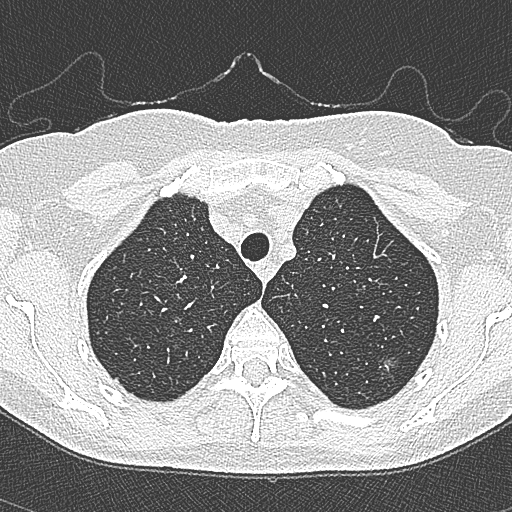
Low-dose screening chest CT, axial slice, second annual screen, lung window (W 1500 / L -600 HU), 1 mm slice thickness, lung (sharp) reconstruction kernel (B80f), 512 × 512 image matrix. Female, age 65 years at enrolment.
Expert reader's lesion annotation, box from (x=365, y=350) to (x=405, y=386) px. The screening reader recorded 4 non-calcified nodules or masses ≥4 mm on this exam; which of them this box marks is not recorded.